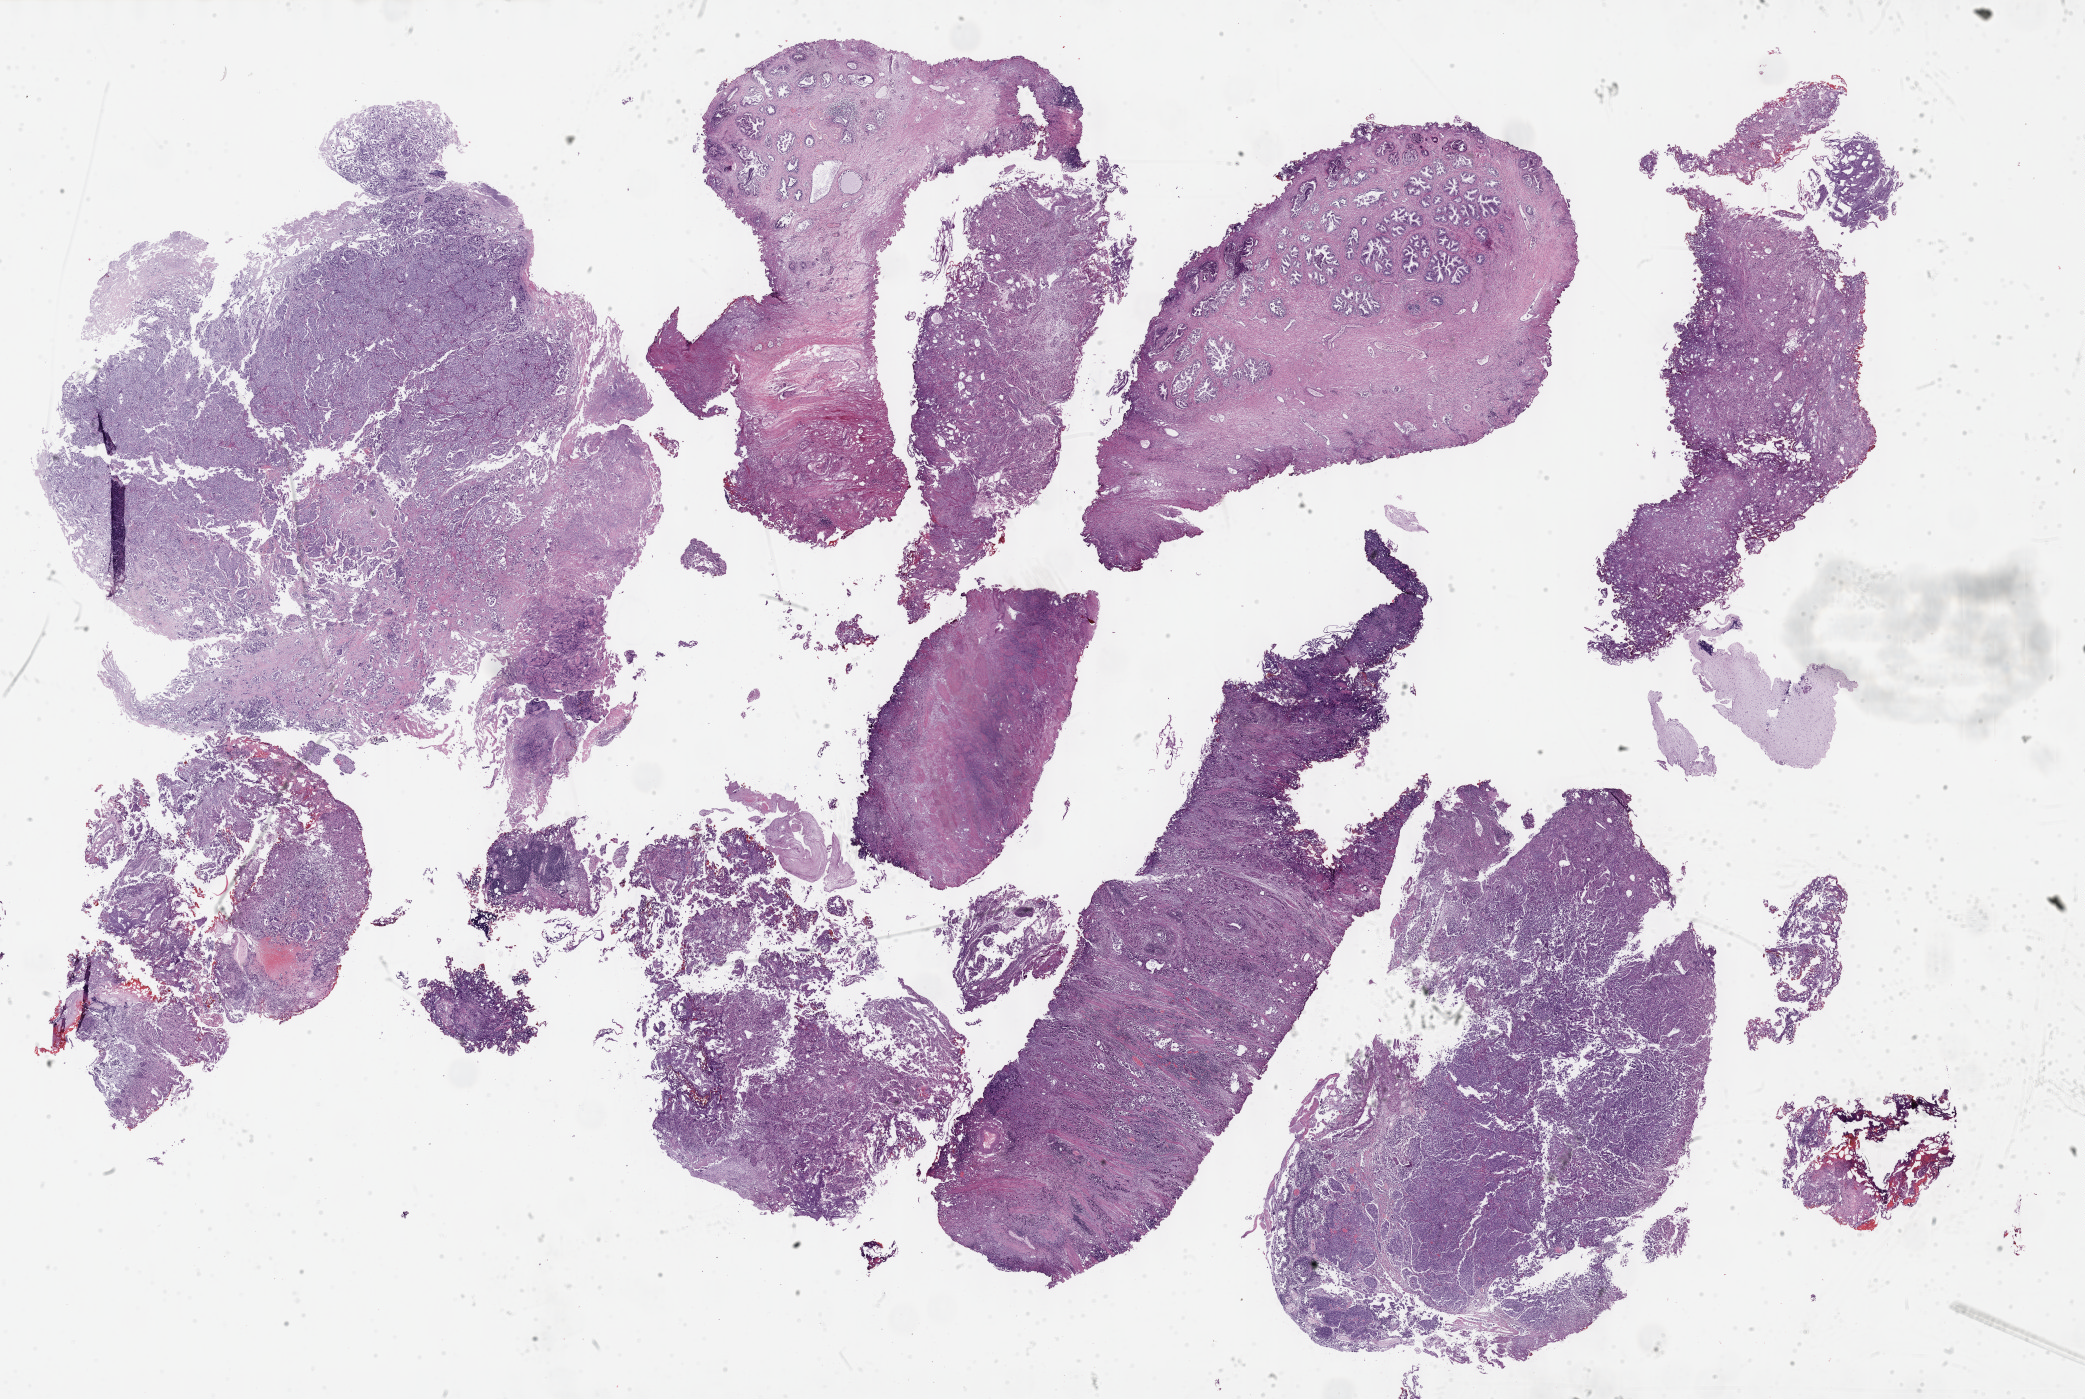
H&E-stained whole-slide image, a low-resolution overview of the entire scanned area, about 33.7 x 22.6 mm (slide scanned at 40x); formalin-fixed paraffin-embedded (FFPE) diagnostic section; bladder, primary tumour sample. Male, age 77 years at initial diagnosis. Histologic grade: high grade.
Pathologic diagnosis: Transitional cell carcinoma. AJCC pathologic stage: IV (7th edition). TNM: T3 N1 M0. Lymph nodes positive (case pathology): 1 of 28 examined.